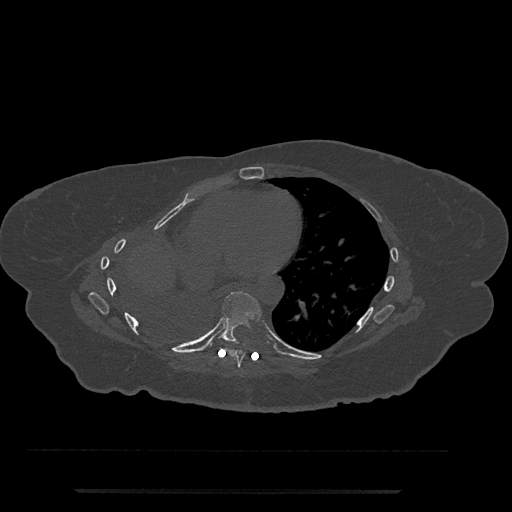
CT including the spine, one axial slice; reconstruction kernel Br40s/3; 120 kVp; bone window (W 1800 / L 400 HU); 0.5 mm slice thickness; 512 × 512 image matrix, field of view 440 × 440 mm. Female patient, age 51 years. Case-level facts recorded for this patient, not image findings: primary cancer: neuro.
Structures marked on this image (semi-automatically segmented with operator editing):
- T7 vertebra: bounding box [x1, y1, x2, y2] px = [224, 349, 245, 368]
- T8 vertebra: [208, 291, 262, 348]